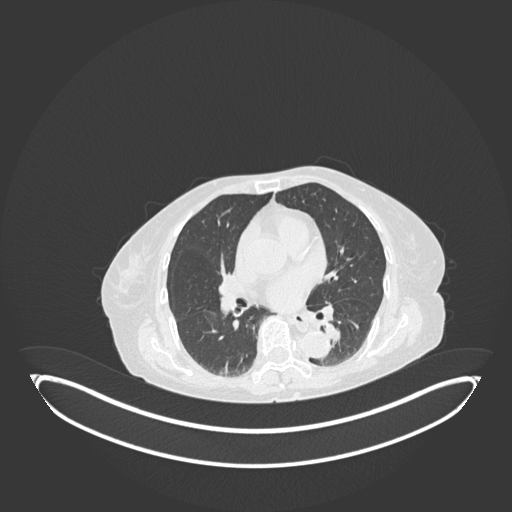
Chest CT, one axial slice; position 63 of 189 along the scan axis; lung window (W 1500 / L -600 HU); 1 mm slice thickness; 512 × 512 image matrix, field of view 500 × 500 mm. Female patient, age 82 years. From the clinical record (not read from this slice): clinical TNM (as recorded): T1b N0 M1.
Structures marked on this image (rectangle marked by the reading radiologist):
- lung tumour (recorded histology: adenocarcinoma): bounding box <322,319,345,345> (left, top, right, bottom; pixels)